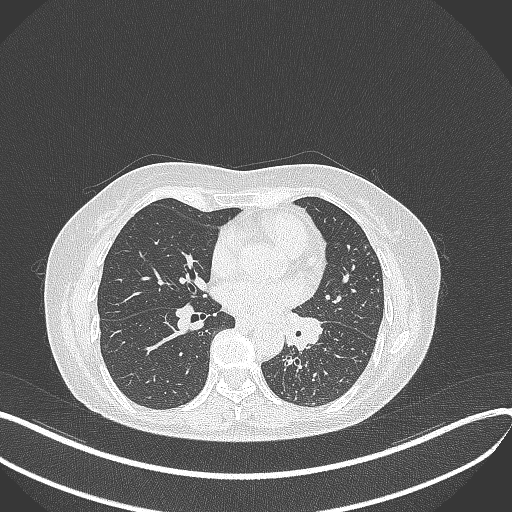
Chest CT, one axial slice. Slice 196 of 429 in the series (ordered by position). 100 kVp. Lung window (W 1500 / L -600 HU). 512 × 512 image matrix. Patient: female, 63 years. Case-level facts recorded for this patient, not image findings: clinical TNM (as recorded): T1b N0 M0; histopathological grade: G2-3.
Outlined on this slice (rectangle marked by the reading radiologist):
- lung tumour (recorded histology: adenocarcinoma): bounding box <284,313,329,351> (left, top, right, bottom; pixels)